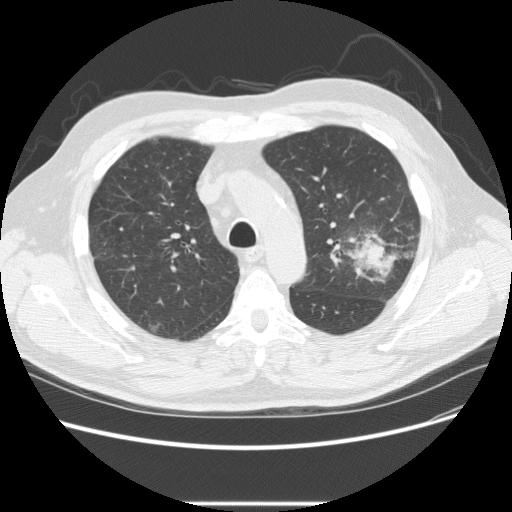
Low-dose screening chest CT, one axial slice. Slice 166 of 233 in the series (ordered by position). Reconstruction kernel STANDARD. 120 kVp. Lung window (W 1500 / L -600 HU). 512 × 512 image matrix, field of view 380 × 380 mm.
Annotated regions visible in this slice (outlined manually by an expert reader):
- lesion 1 (tumor, upper lobe of left lung): bounding box <348,238,398,280> (left, top, right, bottom; pixels)